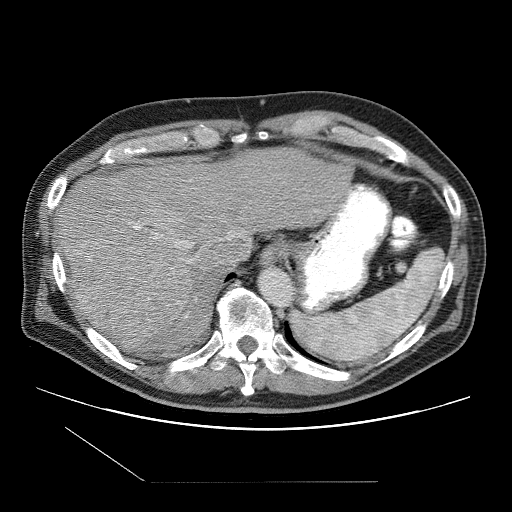
Contrast-enhanced abdominal CT (liver protocol), one axial slice. Position 80 of 109 along the scan axis. Reconstruction kernel STANDARD. One of 2 acquisitions stored at this slice position. Soft-tissue window (W 400 / L 40 HU). 2.5 mm slice thickness. 512 × 512 image matrix, field of view 400 × 400 mm. Case-level facts recorded for this patient, not image findings: diagnosis: hepatocellular carcinoma (patient treated with transarterial chemoembolisation; whether this scan precedes or follows treatment is not stated here); TNM stage (as recorded): Stage-IIIB; Child-Pugh class: A; tumour differentiation: well differentiated; tumour nodularity: multinodular.
Annotated regions visible in this slice (semi-automatically segmented with operator editing):
- liver parenchyma outside the tumour (the mass and vessels are separate outlines, so this box may not span the whole liver): bounding box <56,148,351,352> (left, top, right, bottom; pixels)
- mass: <67,237,194,350>
- liver vessels: <129,222,233,318>